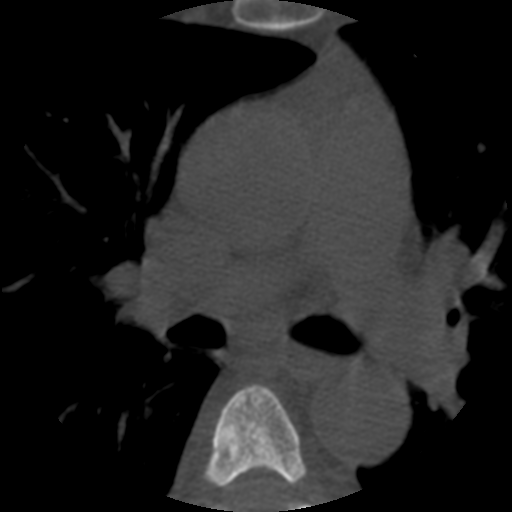
CT including the spine, one axial slice; position 373 of 508 along the scan axis; reconstruction kernel STANDARD; bone window (W 1800 / L 400 HU); 1.25 mm slice thickness; 512 × 512 image matrix, field of view 160 × 160 mm. Patient age 57 years. From the clinical record (not read from this slice): primary cancer: prostate.
Outlined on this slice (semi-automatic segmentation, software-assisted and operator-edited):
- T5 vertebra: bounding box (x1, y1, x2, y2) in pixels: (205, 385, 307, 507)
- T6 vertebra: (211, 501, 309, 512)